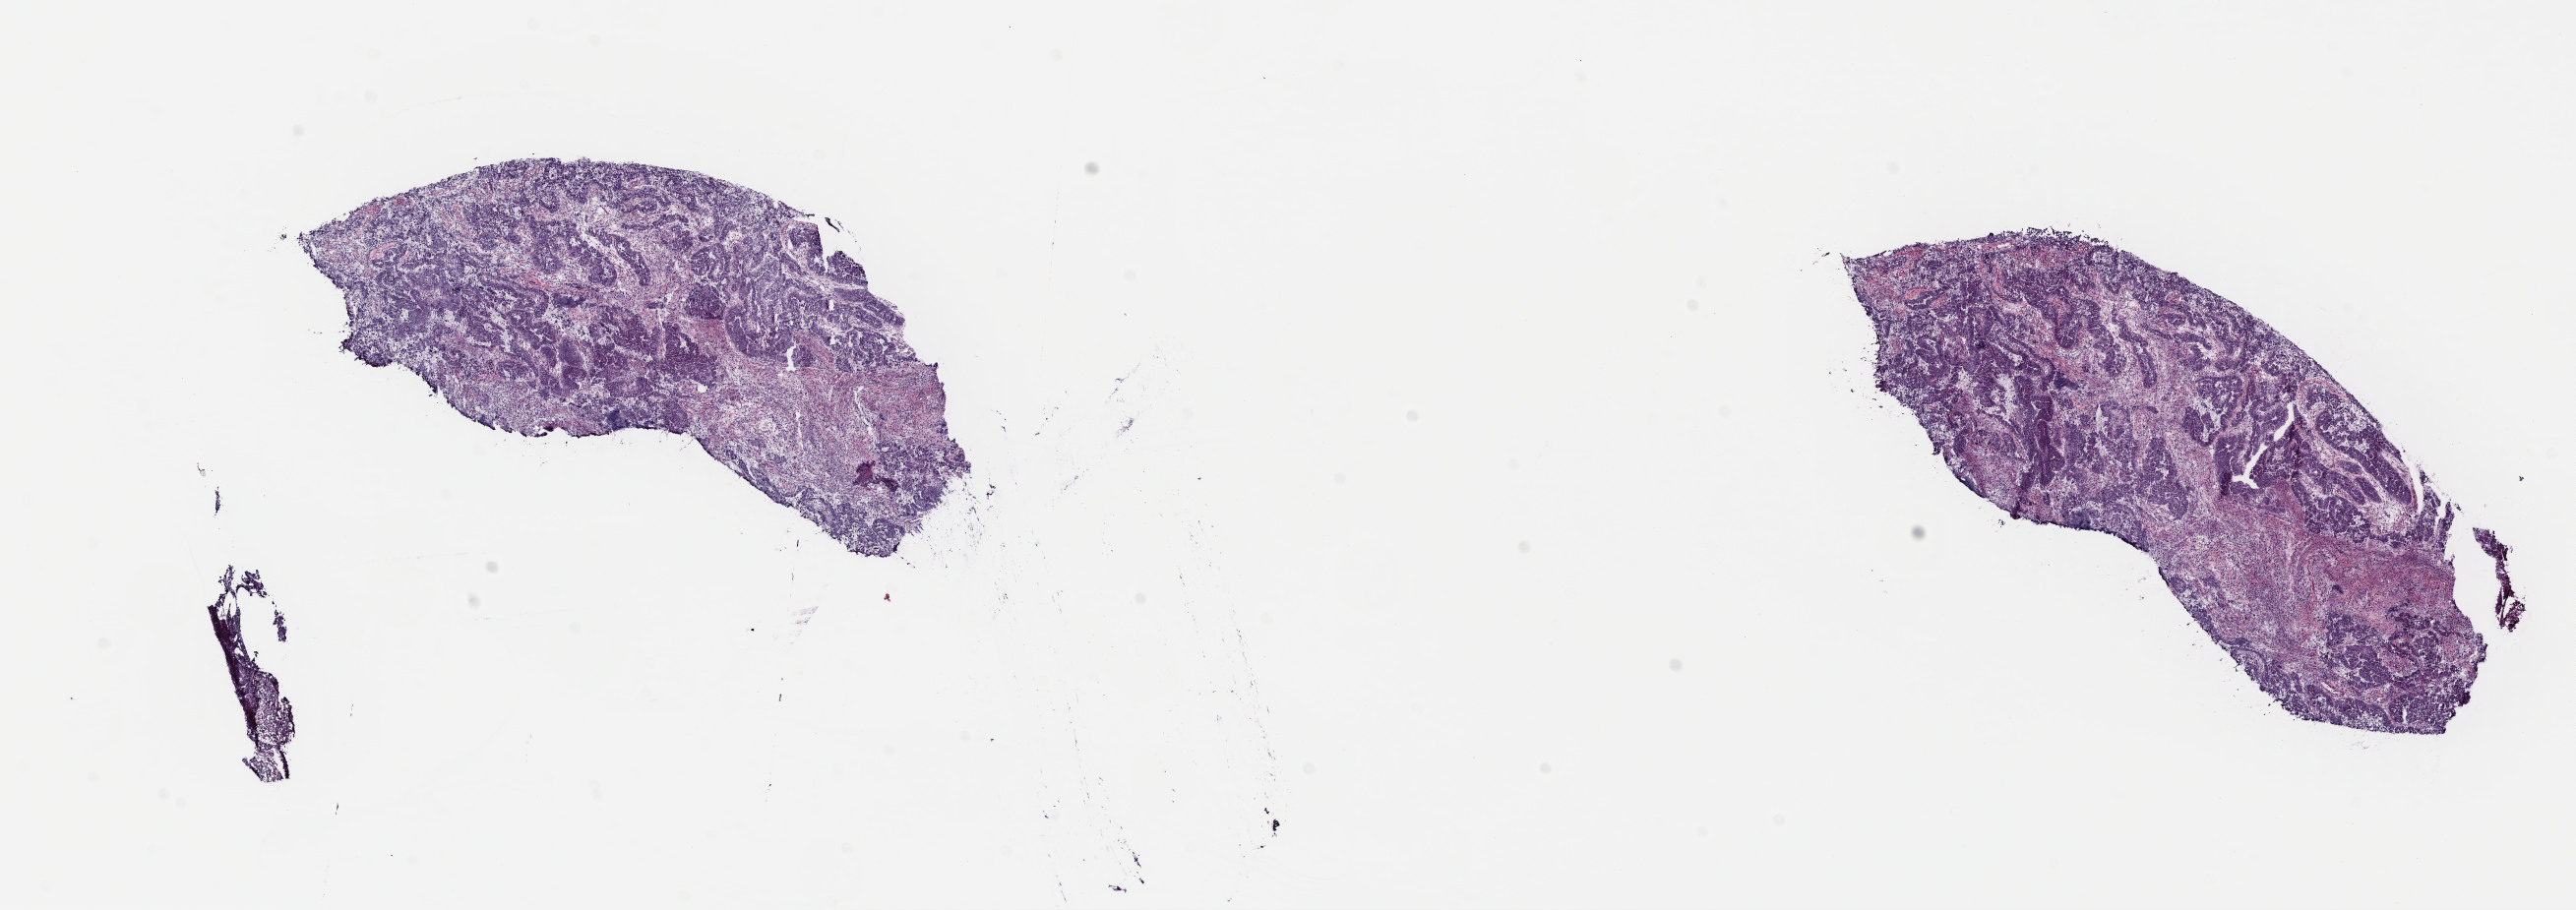
H&E-stained whole-slide image, a low-resolution overview of the entire scanned area, about 20.6 x 7.3 mm, frozen section, sample: primary tumour, uterus. Female, age 67 years at initial diagnosis. Histologic grade: G3 (poorly differentiated). Pathologist review of this section (percent, as recorded): tumour cells 100%, tumour nuclei 65%, normal cells 0%, stromal cells 0%, necrosis 0%. Infiltration values recorded for this section: lymphocyte infiltration 5%, monocyte infiltration 3%, neutrophil infiltration 0%.
Histologic diagnosis: Endometrioid adenocarcinoma, NOS (corpus uteri). FIGO stage: IIIC2.